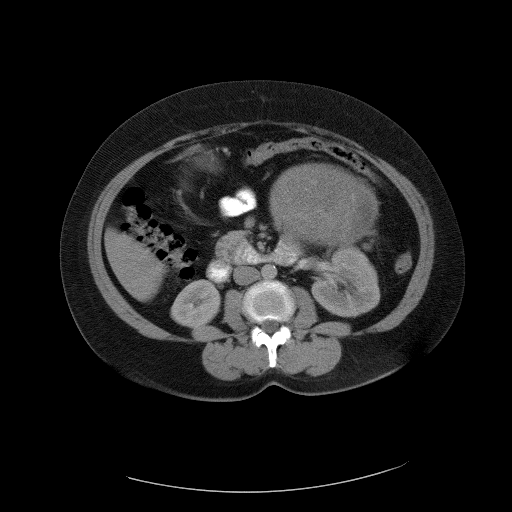
Contrast-enhanced abdominal CT, one axial slice. Position 54 of 90 along the scan axis. 120 kVp. Intravenous contrast given. Soft-tissue window (W 400 / L 40 HU). 5 mm slice thickness. 512 × 512 image matrix, field of view 480 × 480 mm. Female patient, age 55 years. Case-level facts recorded for this patient, not image findings: diagnosis: adrenocortical carcinoma; tumour side: left adrenal; tumour size at pathology: 22 cm; Ki-67 index: 10 %; stage (as recorded): 3.
Outlined on this slice (semi-automatically segmented with operator editing):
- mass: bounding box [x1, y1, x2, y2] px = [272, 164, 376, 243]